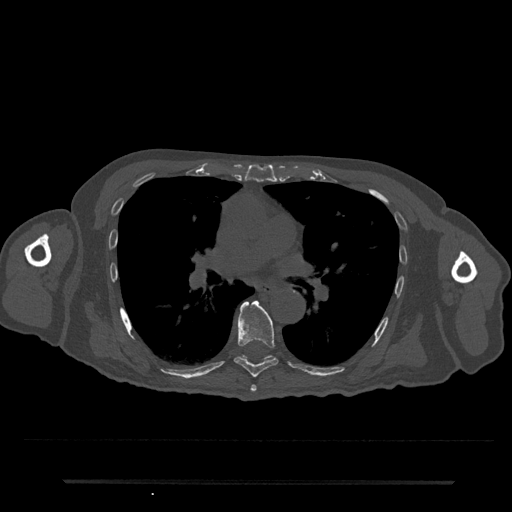
CT including the spine, one axial slice. 120 kVp. Bone window (W 1800 / L 400 HU). 0.5 mm slice thickness. 512 × 512 image matrix, field of view 427 × 427 mm. Patient: male, 74 years. Case-level facts recorded for this patient, not image findings: primary cancer: prostate.
Outlined on this slice (semi-automatically segmented with operator editing):
- T6 vertebra: bounding box [x1, y1, x2, y2] px = [250, 385, 257, 392]
- T7 vertebra: [234, 301, 279, 377]
- T8 vertebra: [241, 355, 274, 362]